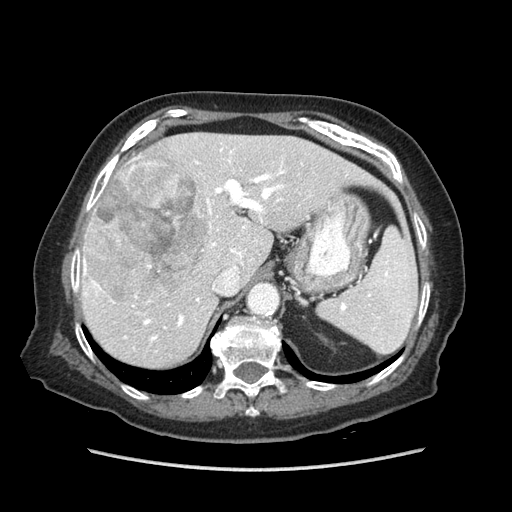
Contrast-enhanced abdominal CT (liver protocol), one axial slice. Position 57 of 89 along the scan axis. Reconstruction kernel STANDARD. Soft-tissue window (W 400 / L 40 HU). 2.5 mm slice thickness. 512 × 512 image matrix, field of view 360 × 360 mm. From the clinical record (not read from this slice): diagnosis: hepatocellular carcinoma (patient treated with transarterial chemoembolisation; whether this scan precedes or follows treatment is not stated here); TNM stage (as recorded): Stage-IIIA; Child-Pugh class: A; tumour nodularity: multinodular; tumour size: 11 cm.
Annotated regions visible in this slice (semi-automatically segmented with operator editing):
- liver parenchyma outside the tumour (the mass and vessels are separate outlines, so this box may not span the whole liver): bounding box <76,132,378,368> (left, top, right, bottom; pixels)
- mass: <85,160,206,301>
- liver vessels: <77,148,303,341>